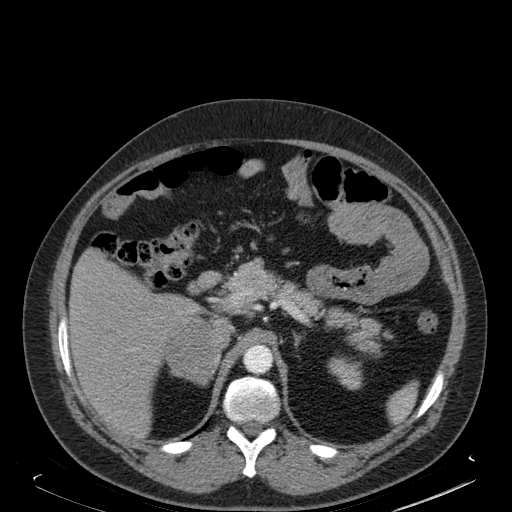
Contrast-enhanced abdominal CT, one axial slice. Slice 116 of 181 in the series (ordered by position). Soft-tissue window (W 400 / L 40 HU). 512 × 512 image matrix, field of view 405 × 405 mm. Male patient. From the clinical record (not read from this slice): diagnosis: adrenocortical carcinoma; tumour side: right adrenal; tumour size at pathology: 7.5 cm; Ki-67 index: 25 %.
Outlined on this slice (semi-automatic segmentation, software-assisted and operator-edited):
- mass: box from (x=165, y=316) to (x=219, y=385) px